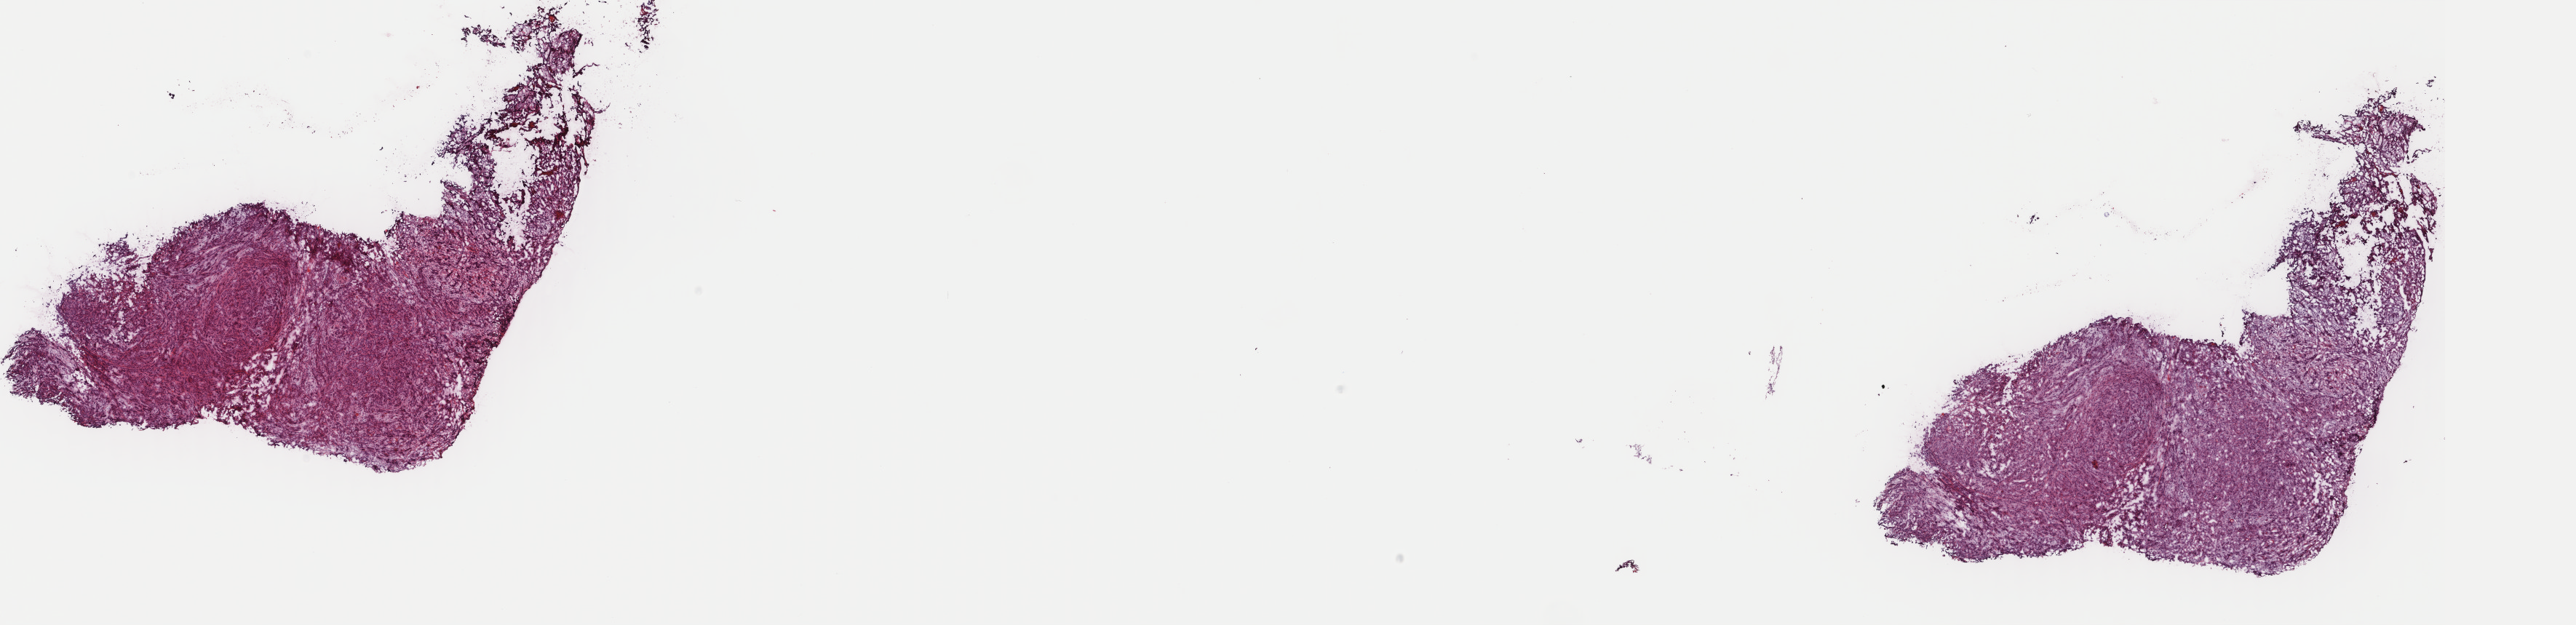
Hematoxylin and eosin (H&E) stained whole-slide image — whole scanned area (about 28.1 x 6.8 mm) shown as a low-resolution overview. Frozen section. Sample: primary tumour, head and neck. Patient: male, age at initial diagnosis 69 years. Histologic grade: G2 (moderately differentiated). Composition of this section per pathologist review: tumour cells 100%, tumour nuclei 75%, normal cells 0%, stromal cells 0%, necrosis 0%. Infiltration values recorded for this section: lymphocyte infiltration 4%, monocyte infiltration 0%, neutrophil infiltration 0%.
Pathologic diagnosis: Squamous cell carcinoma, NOS (cheek mucosa). AJCC pathologic stage: III. Laterality: right.